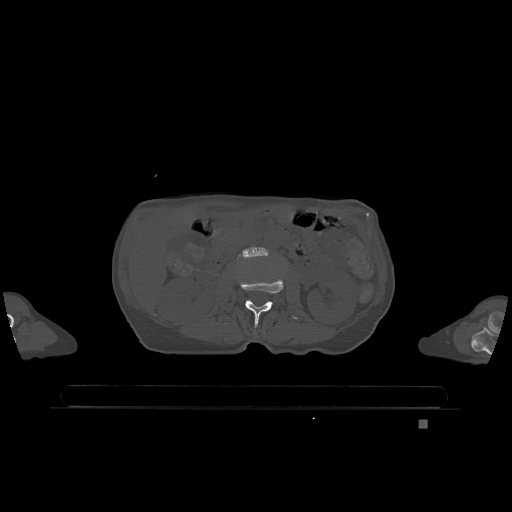
CT including the spine, one axial slice; position 404 of 1317 along the scan axis; bone window (W 1800 / L 400 HU); 0.5 mm slice thickness; 512 × 512 image matrix, field of view 500 × 500 mm. Female patient, age 74 years. From the clinical record (not read from this slice): primary cancer: lung; vertebrae with lytic lesions (as recorded): T1, T4, T5, T6, L4, L5.
Annotated regions visible in this slice (semi-automatic segmentation, software-assisted and operator-edited):
- L2 vertebra: bounding box [x1, y1, x2, y2] px = [240, 279, 298, 327]
- L3 vertebra: [243, 246, 268, 258]